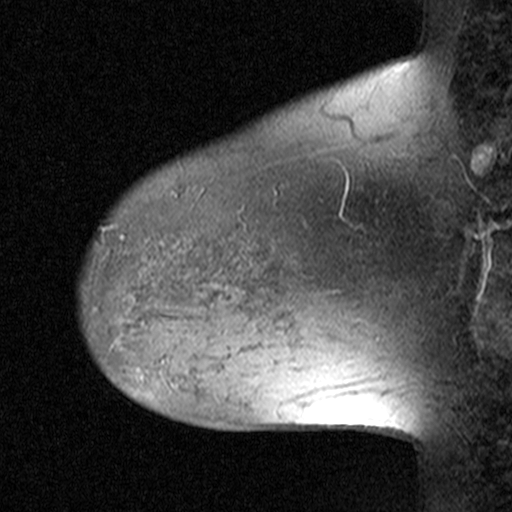
Breast MRI (dynamic contrast-enhanced), one sagittal slice. Slice 34 of 44 in the series (ordered by position). Dynamic contrast-enhanced study with each time point stored as its own series, time point 2 of 3 at this slice position (early post-contrast, ordered by acquisition time). 1.5 T. TE 4.5 ms, TR 11 ms. 512 × 512 image matrix. Patient: female, 38 years. From the clinical record (not read from this slice): setting: breast cancer imaged before/during neoadjuvant chemotherapy; receptor status: HR-positive, HER2-negative.
Annotated regions visible in this slice (semi-automatically segmented with operator editing):
- analysis volume of interest (the breast-tissue region the enhancement analysis was run in; not a lesion): bounding box <152,236,253,335> (left, top, right, bottom; pixels)
- tumour enhancement mask (voxels above the 90 % enhancement threshold inside the analysis volume of interest): <224,286,227,289>